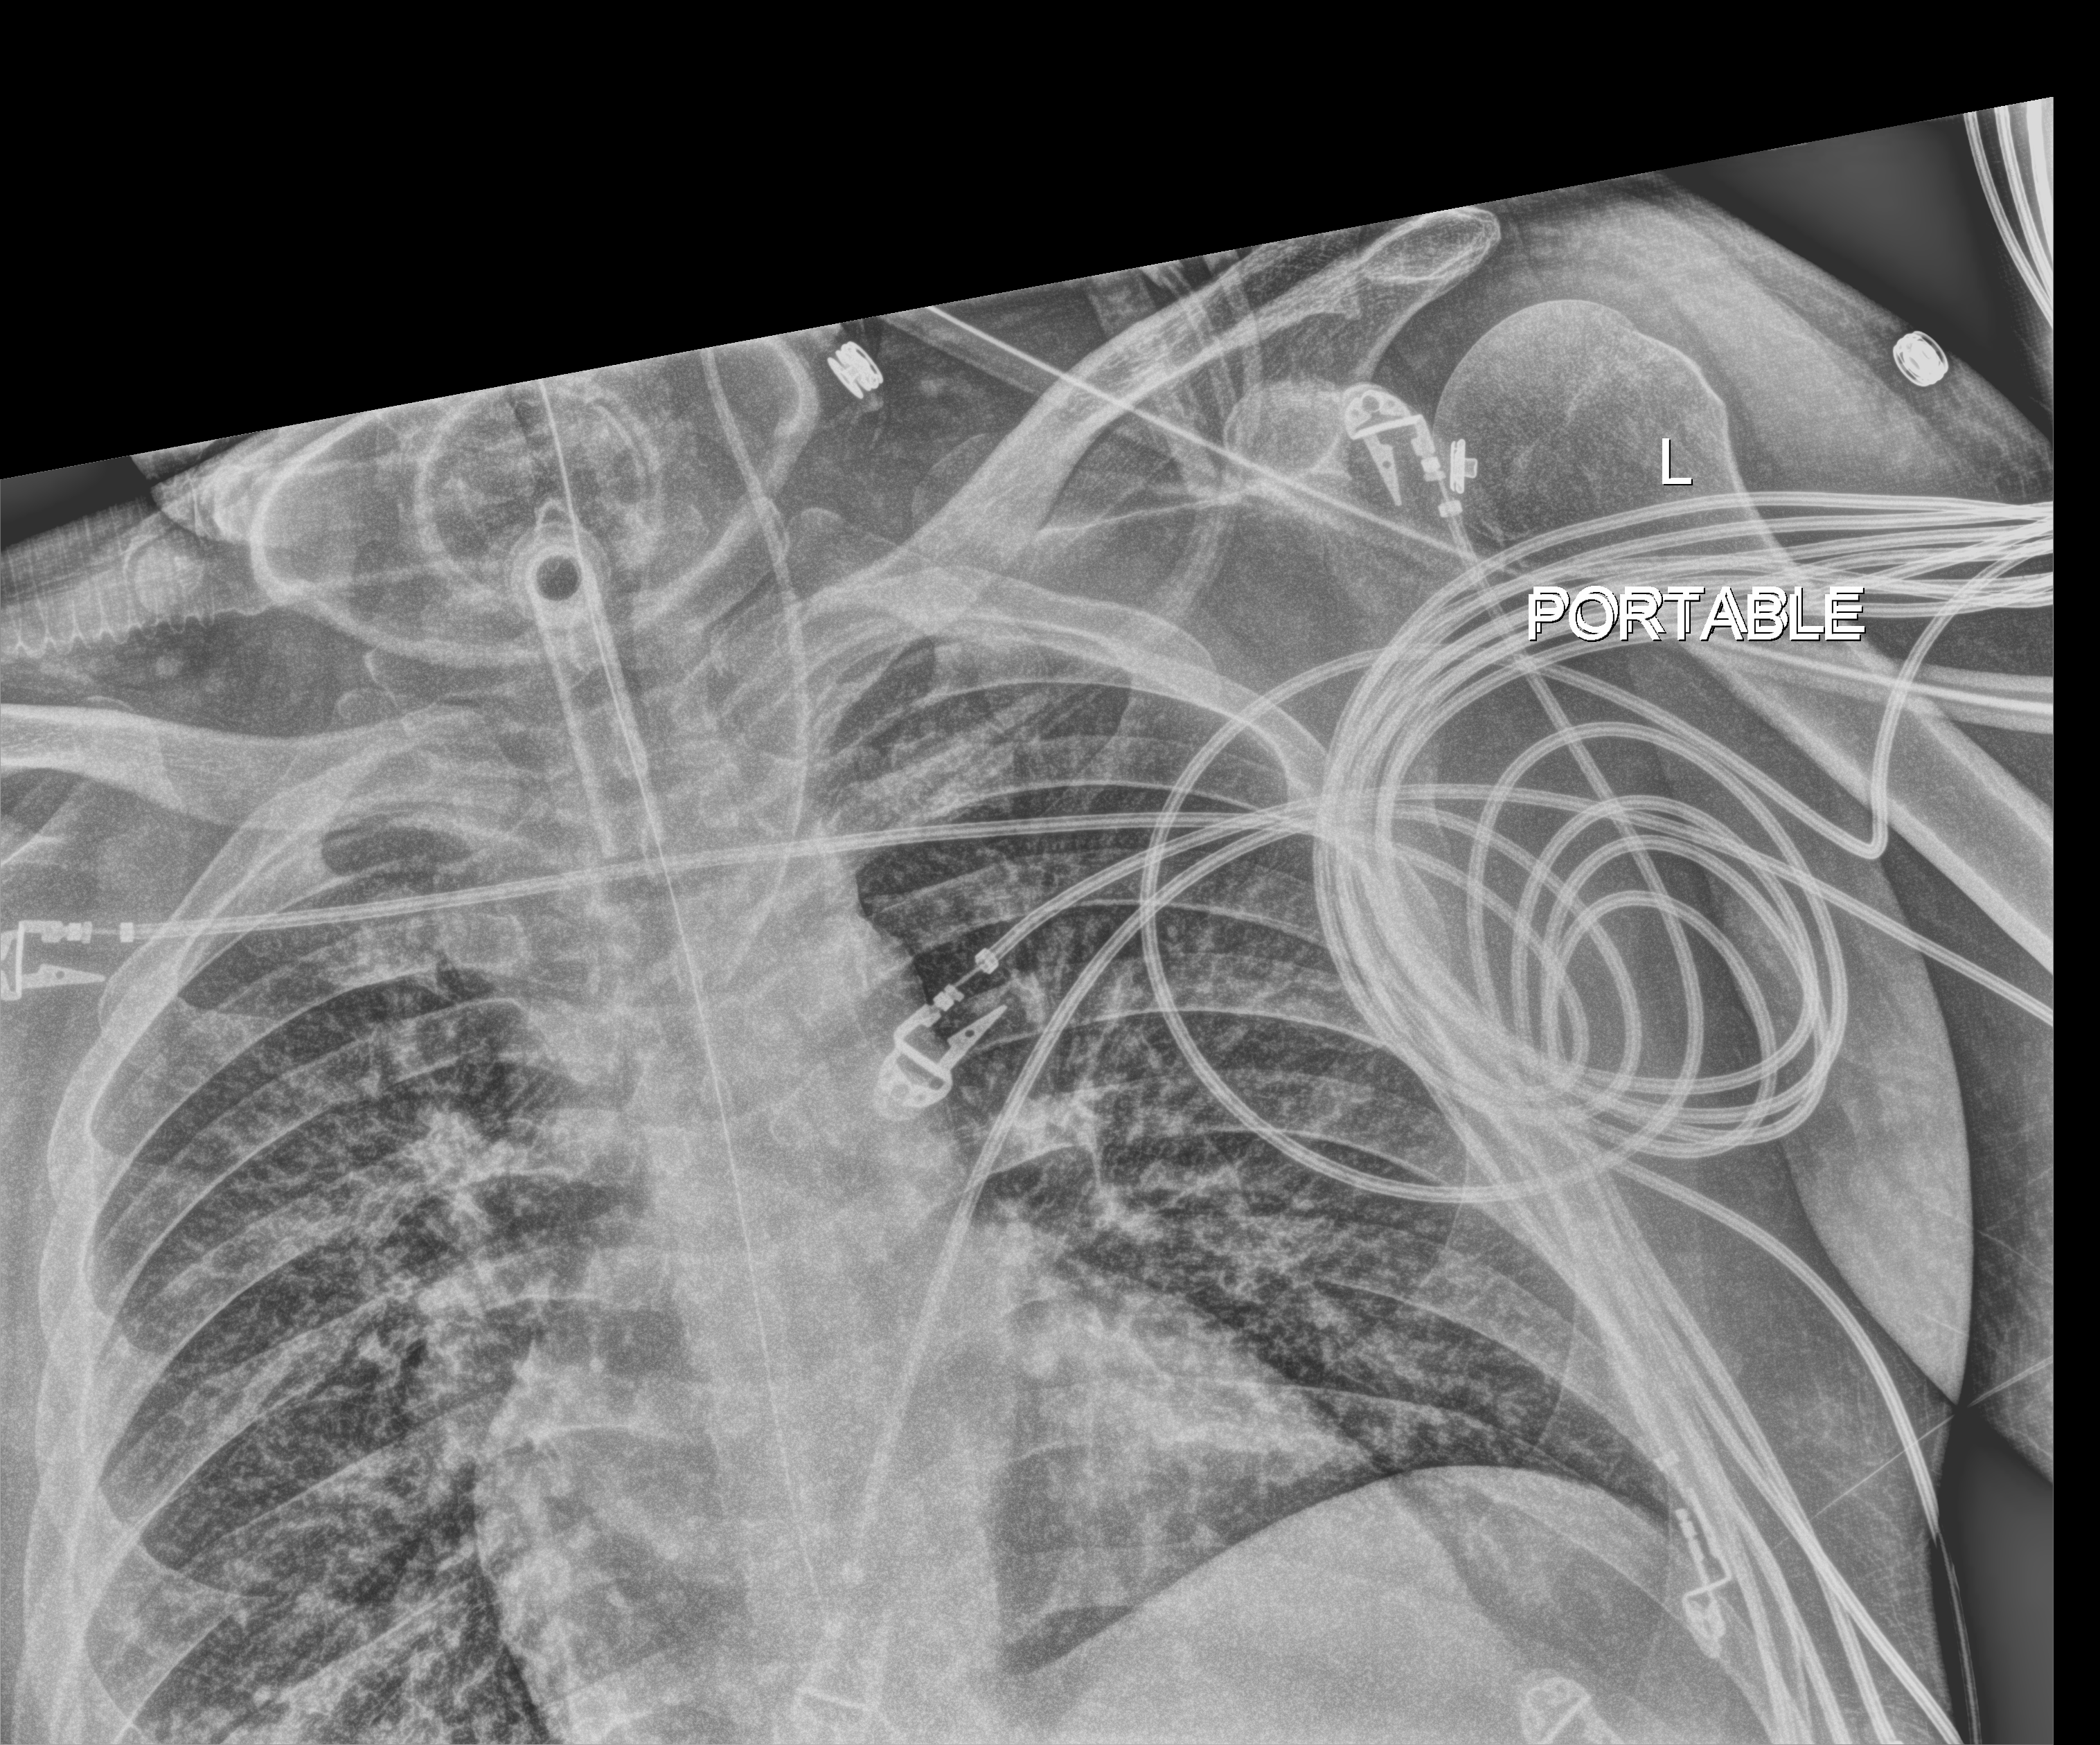
Bedside chest radiograph (digital radiography), anteroposterior (AP) projection. Patient hospitalised with COVID-19; female, aged 75–90 years.
From the hospital-stay record, not from the radiograph (when in the stay this image was taken is not recorded):
- smoking status (admission record): former